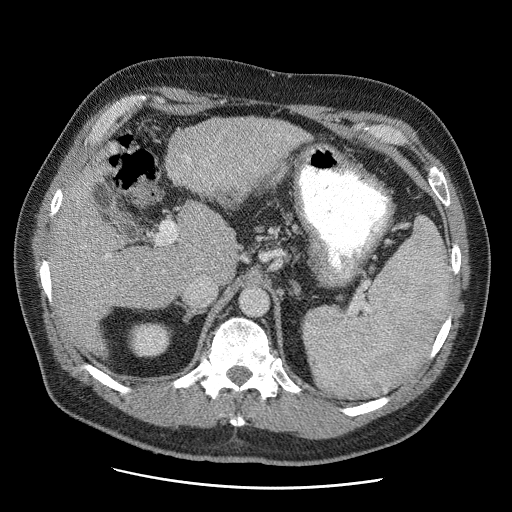
Contrast-enhanced abdominal CT (liver protocol), one axial slice. Slice 30 of 81 in the series (ordered by position). Reconstruction kernel STANDARD. 120 kVp. Soft-tissue window (W 400 / L 40 HU). 512 × 512 image matrix, field of view 380 × 380 mm. From the clinical record (not read from this slice): diagnosis: hepatocellular carcinoma (patient treated with transarterial chemoembolisation; whether this scan precedes or follows treatment is not stated here); TNM stage (as recorded): Stage-IIIA; Child-Pugh class: A; tumour differentiation: moderately differentiated.
Annotated regions visible in this slice (semi-automatically segmented with operator editing):
- abdominal aorta: bounding box [x1, y1, x2, y2] px = [239, 287, 268, 317]
- liver parenchyma outside the tumour (the mass and vessels are separate outlines, so this box may not span the whole liver): [50, 116, 308, 348]